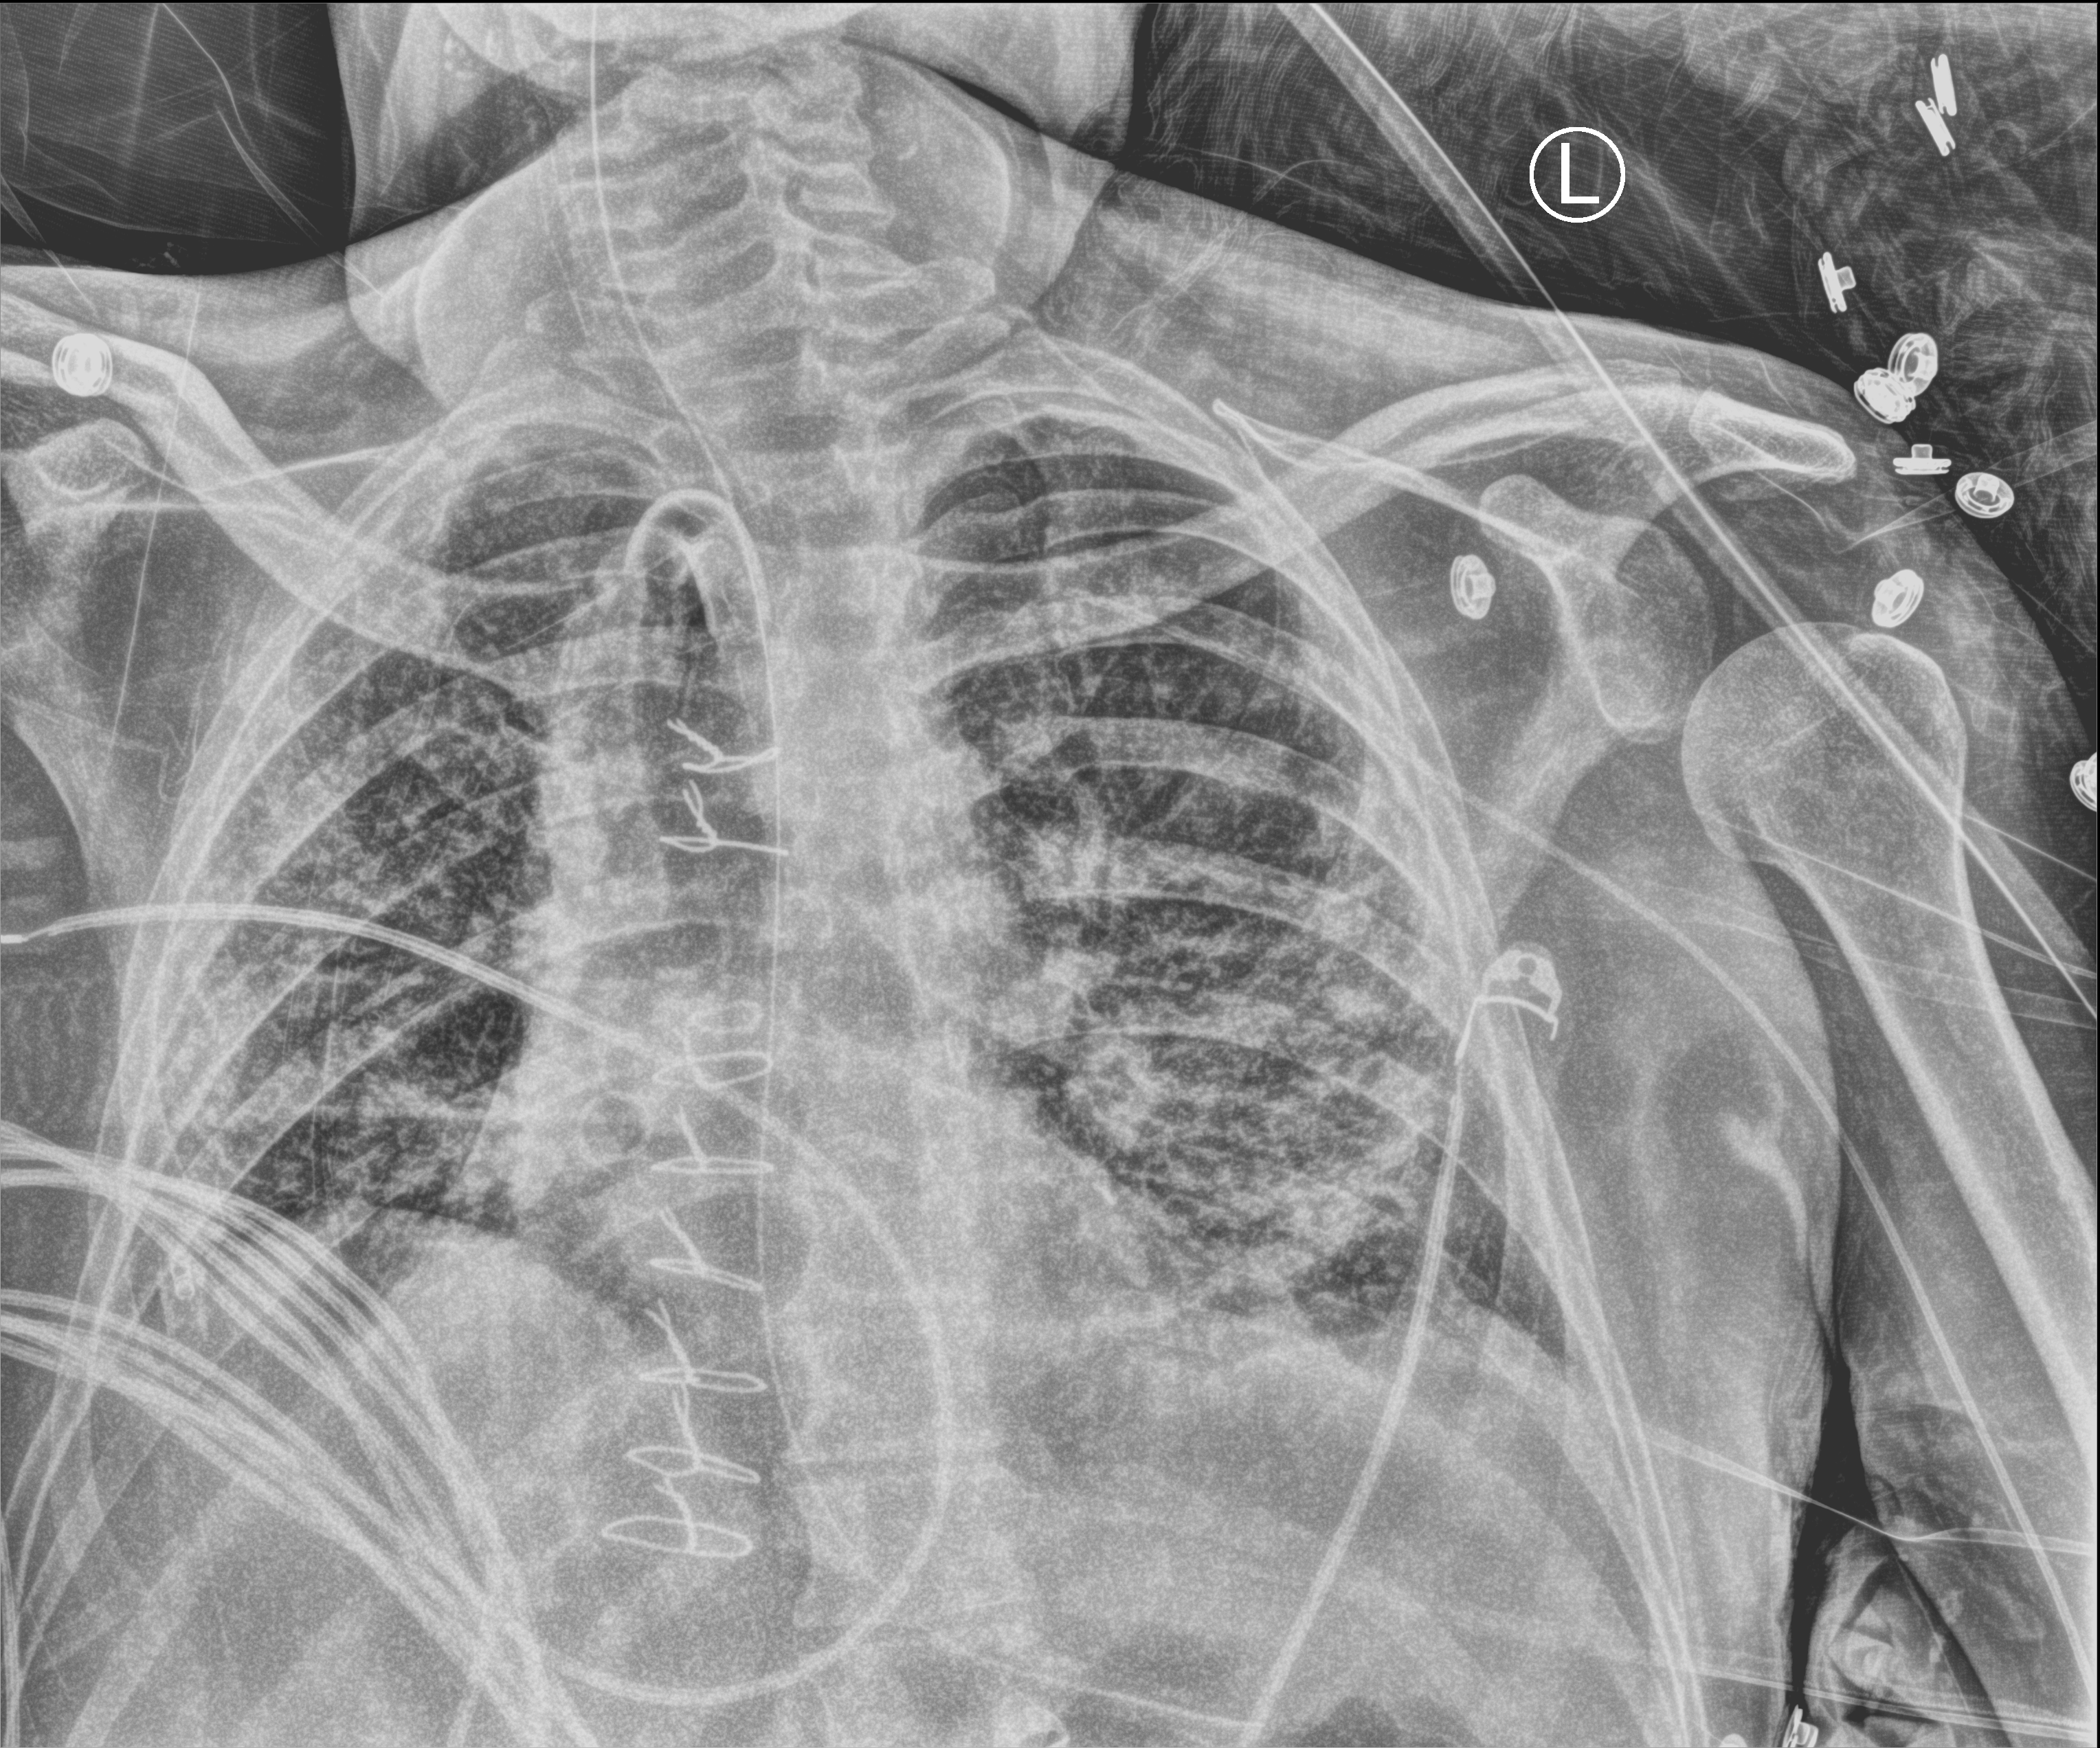
Portable chest radiograph; anteroposterior (AP) projection. Male patient hospitalised with COVID-19, age 18–59 years.
From the hospital-stay record, not from the radiograph (when in the stay this image was taken is not recorded):
- mechanically ventilated during this hospital stay: yes